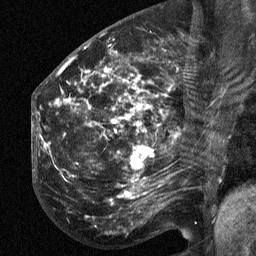
Breast MRI (dynamic contrast-enhanced), one sagittal slice; slice 29 of 64 in the series (ordered by position); dynamic contrast-enhanced study with each time point stored as its own series, time point 2 of 3 at this slice position (early post-contrast, ordered by acquisition time); 1.5 T; TE 4.8 ms, TR 27 ms; 256 × 256 image matrix, field of view 200 × 200 mm. Female patient, age 50 years. Case-level facts recorded for this patient, not image findings: setting: breast cancer imaged before/during neoadjuvant chemotherapy; receptor status: HER2-positive.
Outlined on this slice (semi-automatic segmentation, software-assisted and operator-edited):
- analysis volume of interest (the breast-tissue region the enhancement analysis was run in; not a lesion): bounding box [x1, y1, x2, y2] px = [53, 64, 211, 216]
- tumour enhancement mask (voxels above the 90 % enhancement threshold inside the analysis volume of interest): [105, 69, 150, 170]